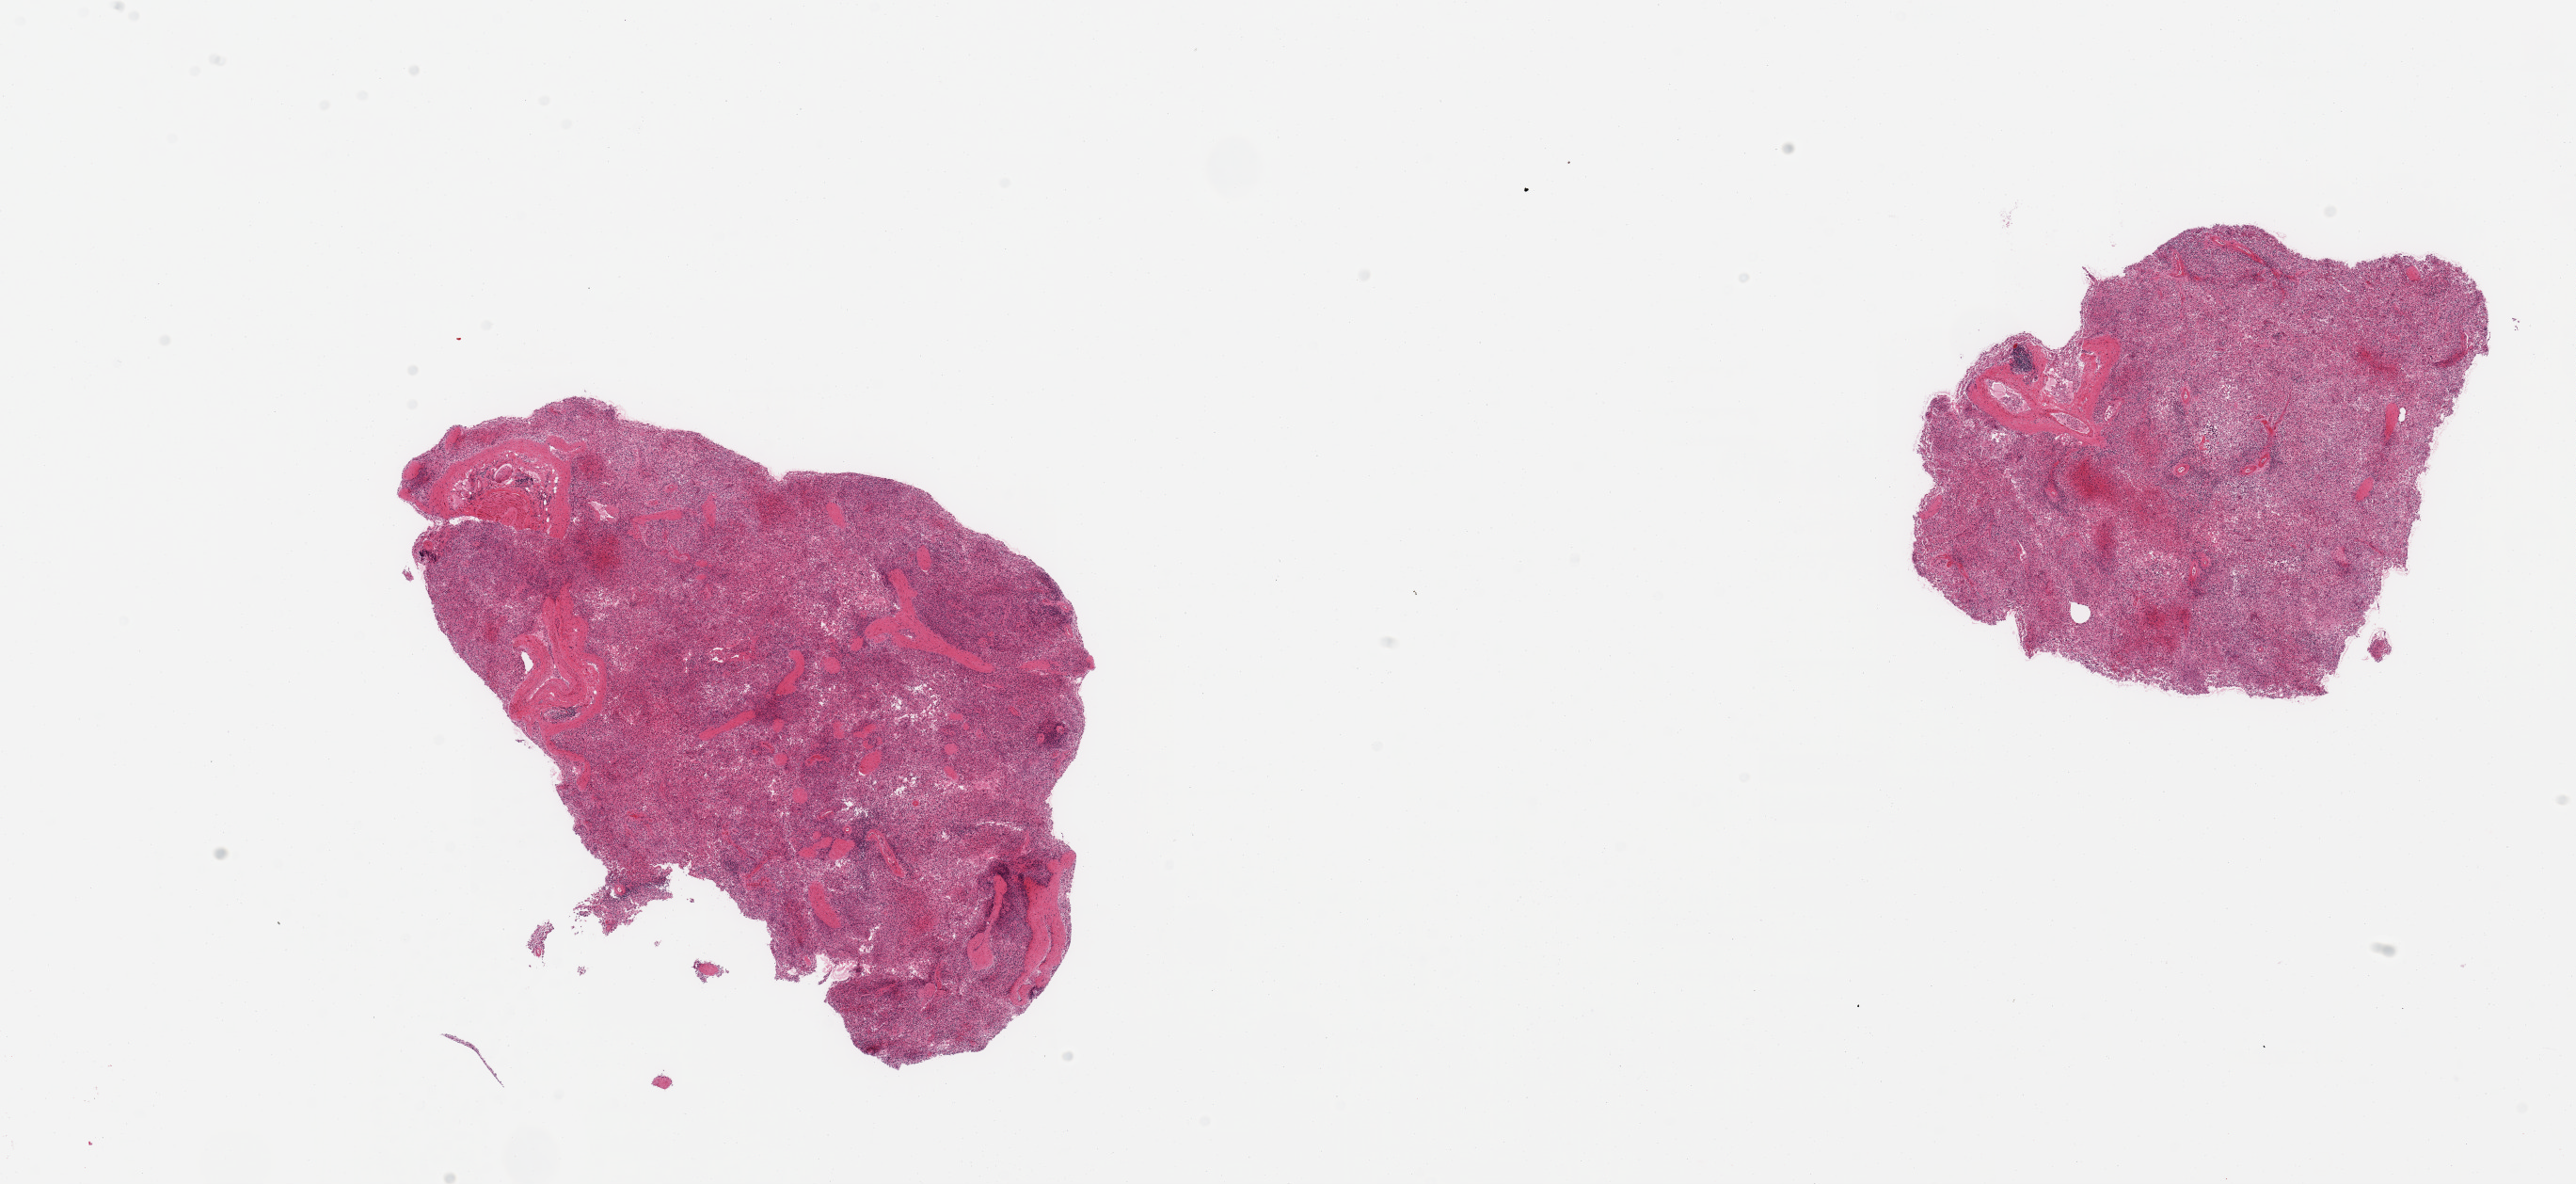
Hematoxylin and eosin (H&E) whole-slide image, whole scanned area (about 21.7 x 10.0 mm) shown as a low-resolution overview. PAXgene-fixed paraffin-embedded (PFPE) section. Section of spleen (target tissue). Tissue donor sample. Female donor.
Review note (as recorded): 2 pieces; no congestion; low lymphoid content.